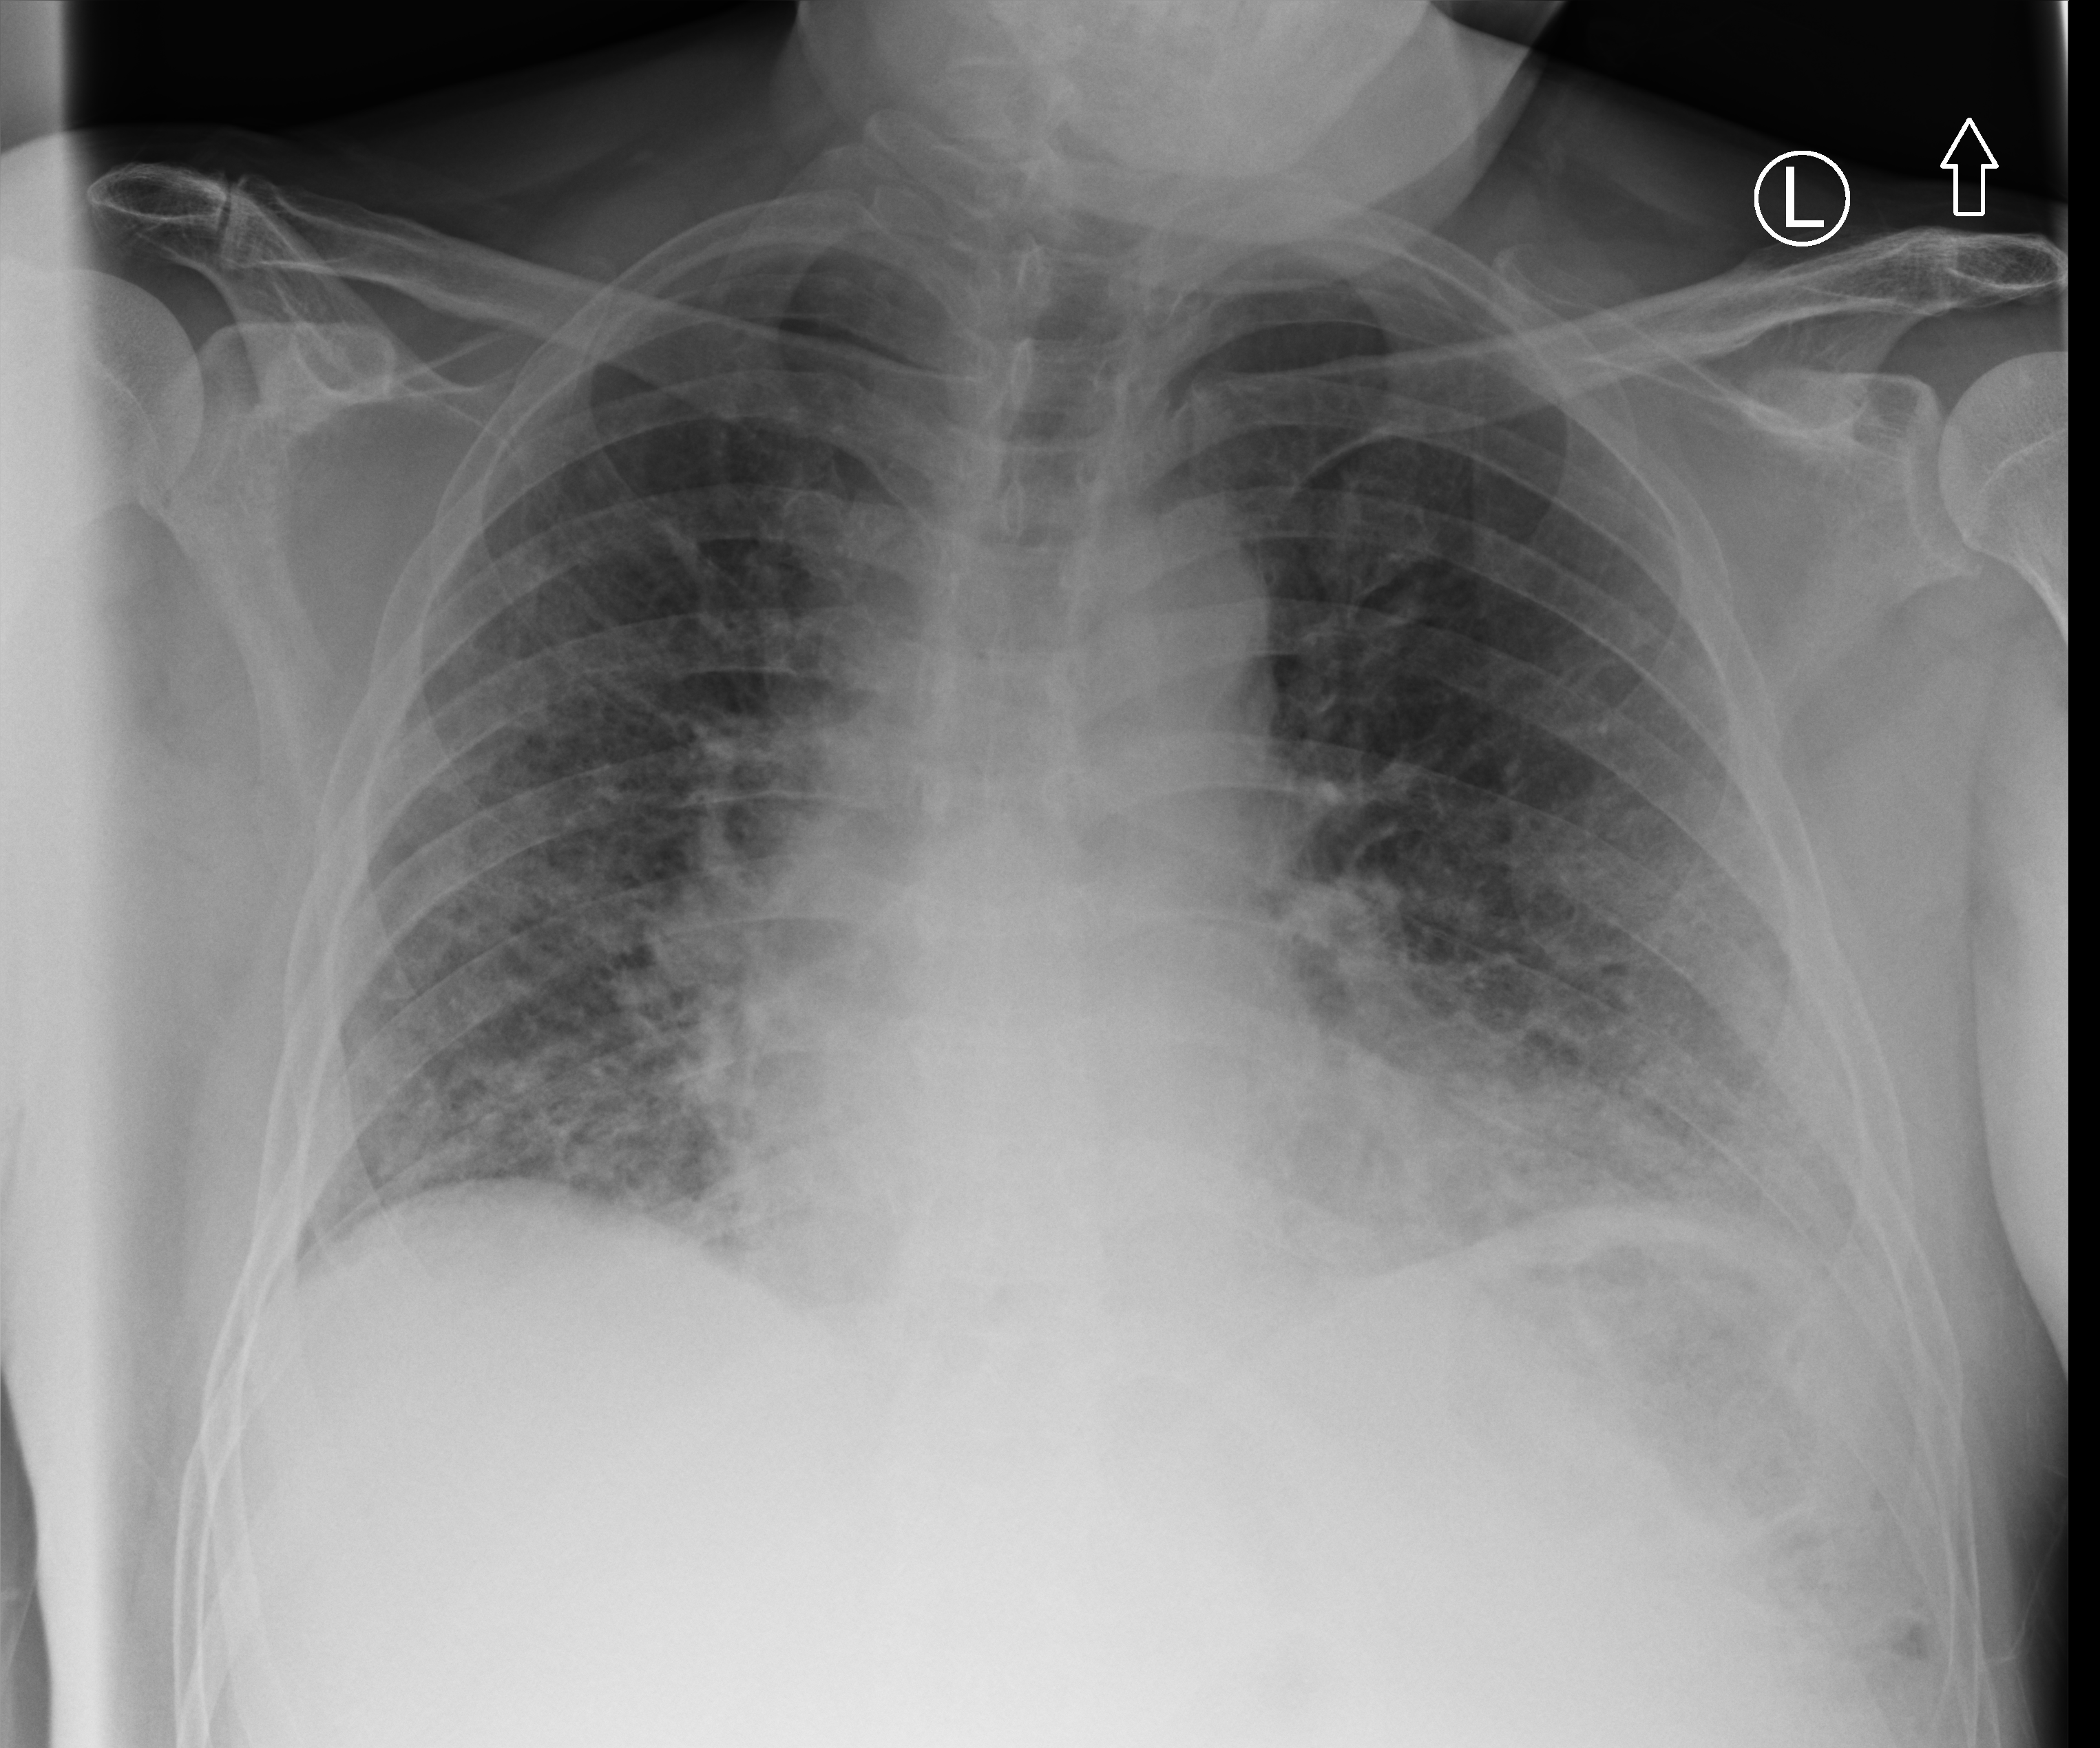
Chest X-ray (portable), anteroposterior (AP) projection. Male patient hospitalised with COVID-19, age 60–74 years.
From the hospital-stay record, not from the radiograph (when in the stay this image was taken is not recorded):
- mechanically ventilated during this hospital stay: yes